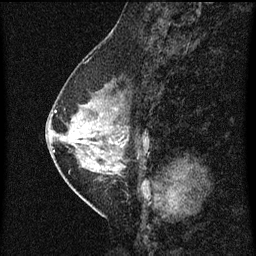
Breast MRI (dynamic contrast-enhanced), one sagittal slice. Position 27 of 60 along the scan axis. Dynamic contrast-enhanced series, image 2 of 3 at this slice position (ordered by acquisition). 1.5 T. TE 4.2 ms, TR 8 ms. 256 × 256 image matrix, field of view 180 × 180 mm. Patient: female, 47 years.
Annotated regions visible in this slice (semi-automatically segmented with operator editing):
- analysis volume of interest (the breast-tissue region the enhancement analysis was run in; not a lesion): bounding box [x1, y1, x2, y2] px = [54, 80, 146, 187]
- tumour enhancement mask (voxels above the 70 % enhancement threshold inside the analysis volume of interest): [54, 112, 120, 159]